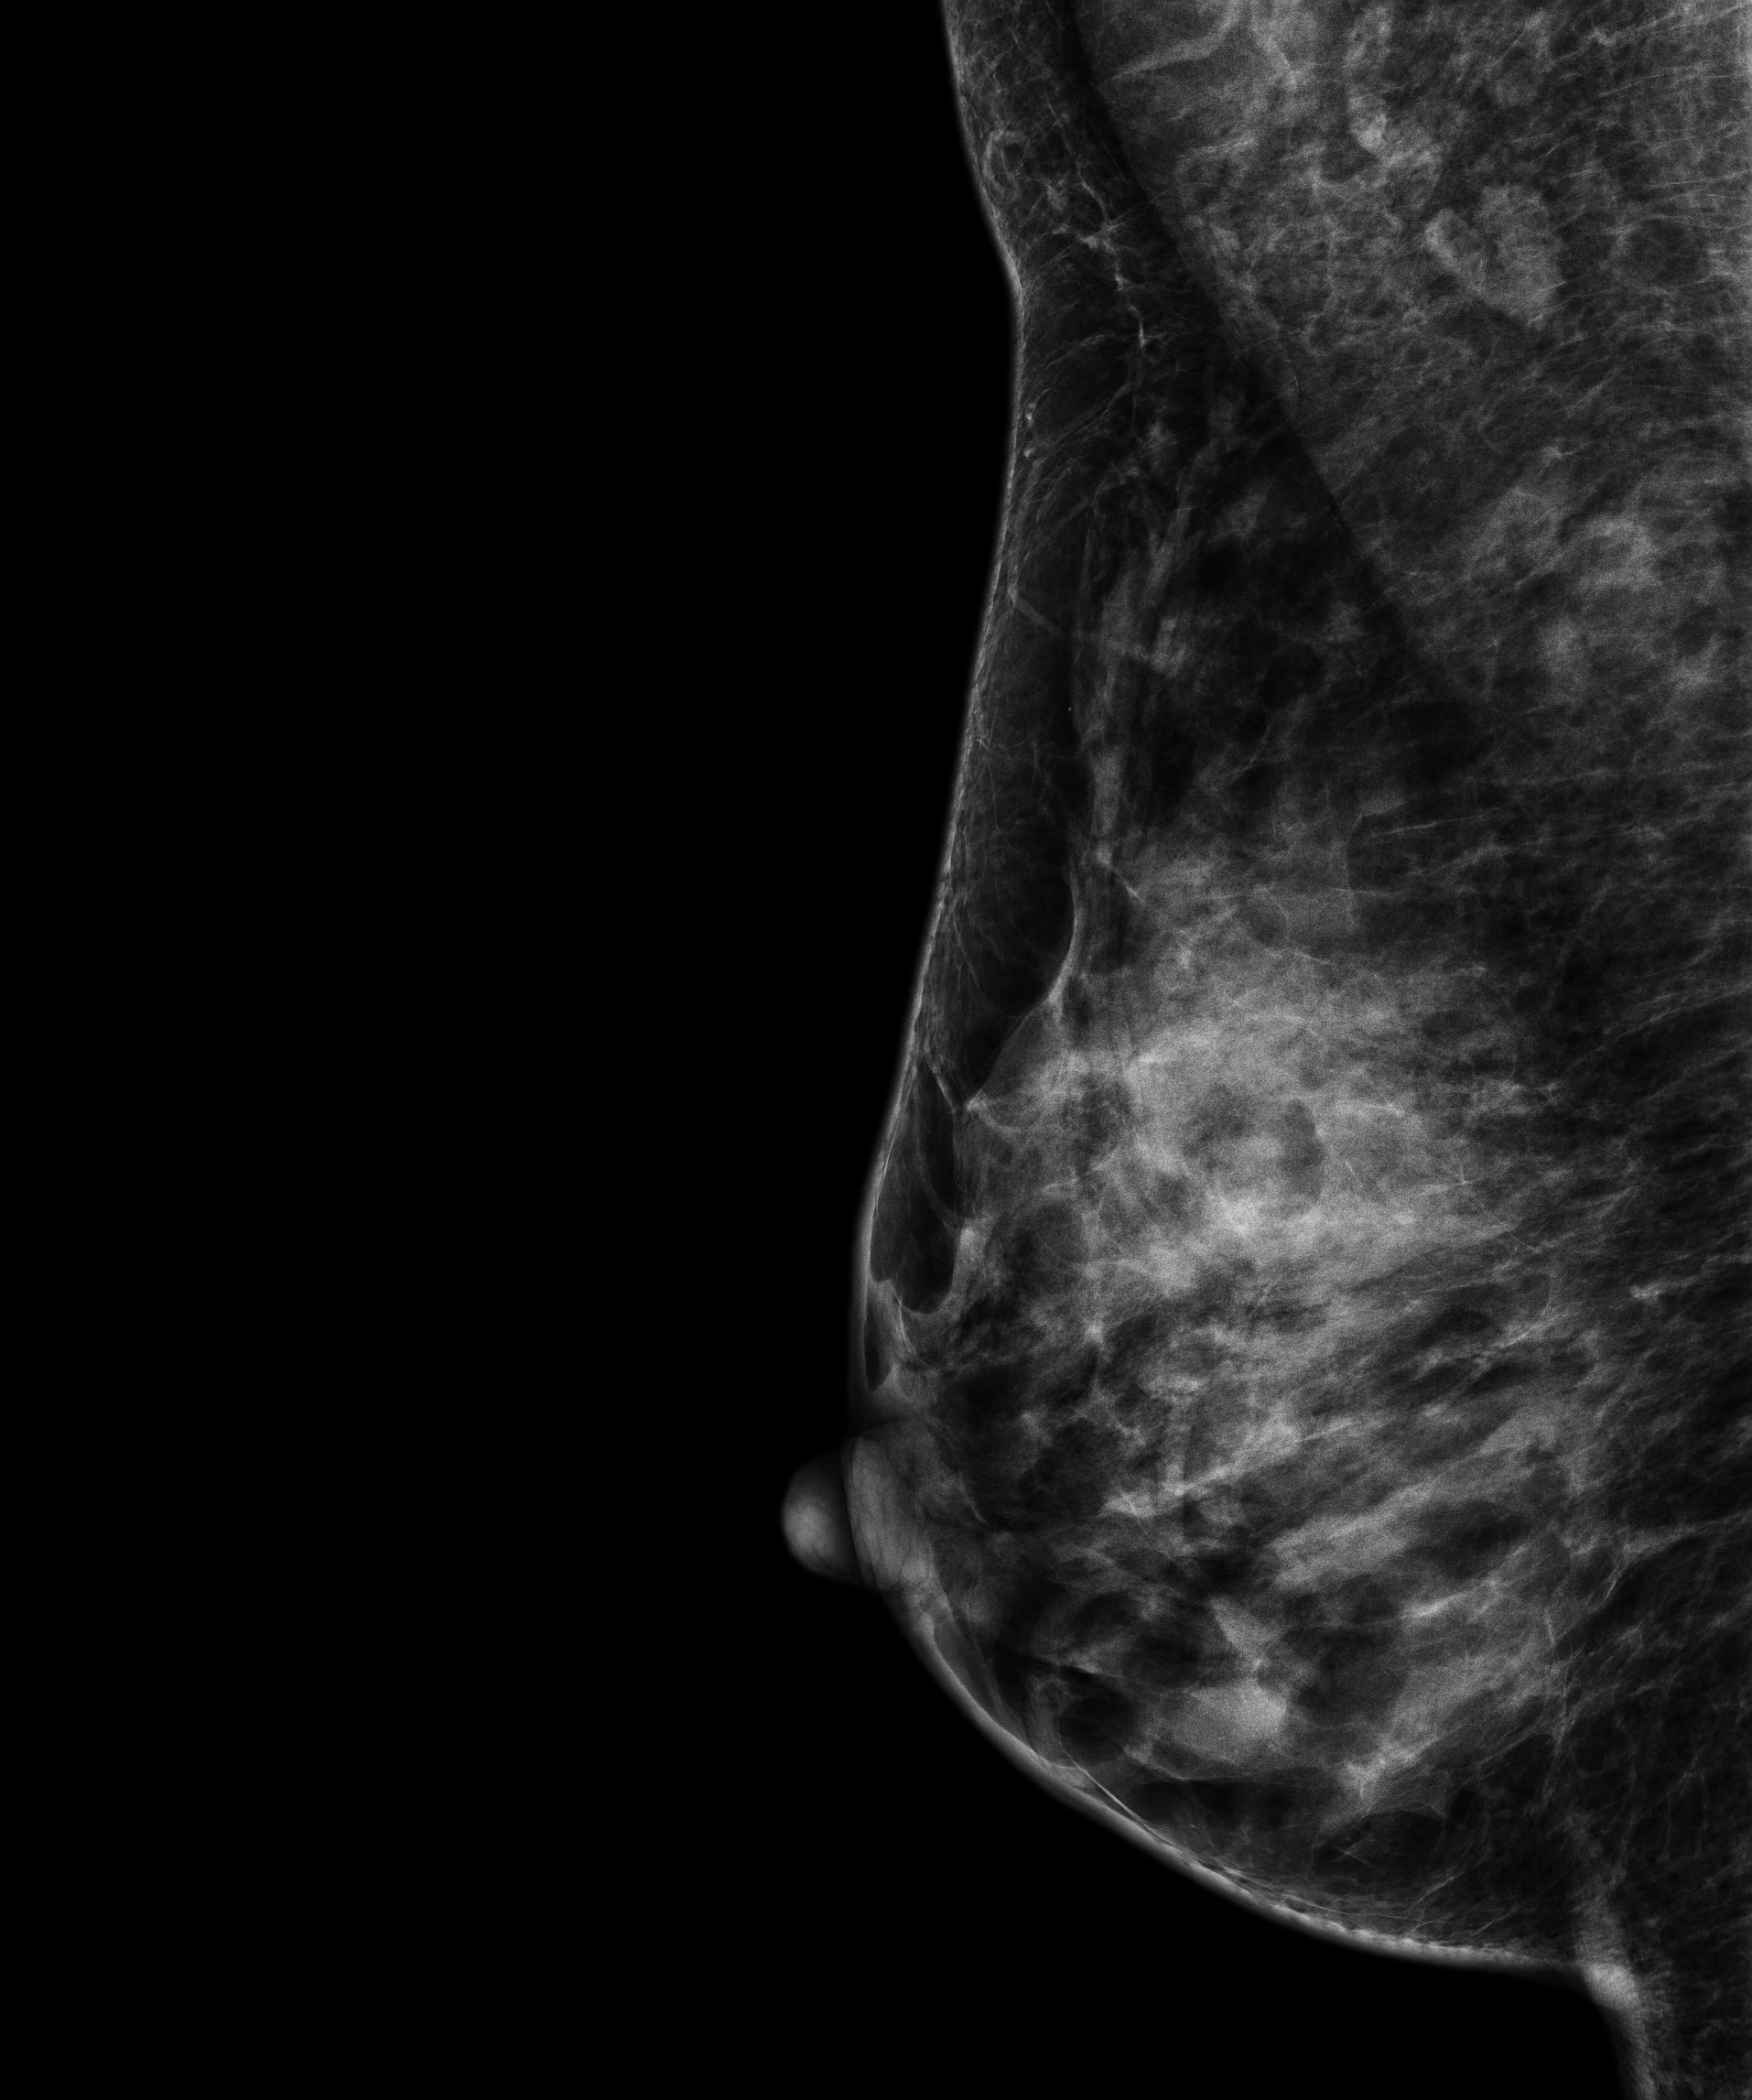
Screening examination, compressed breast thickness 47.6 mm. Patient aged 56 years (female).
Image type: full-field digital mammogram. Breast: right. Projection: medio-lateral oblique projection.